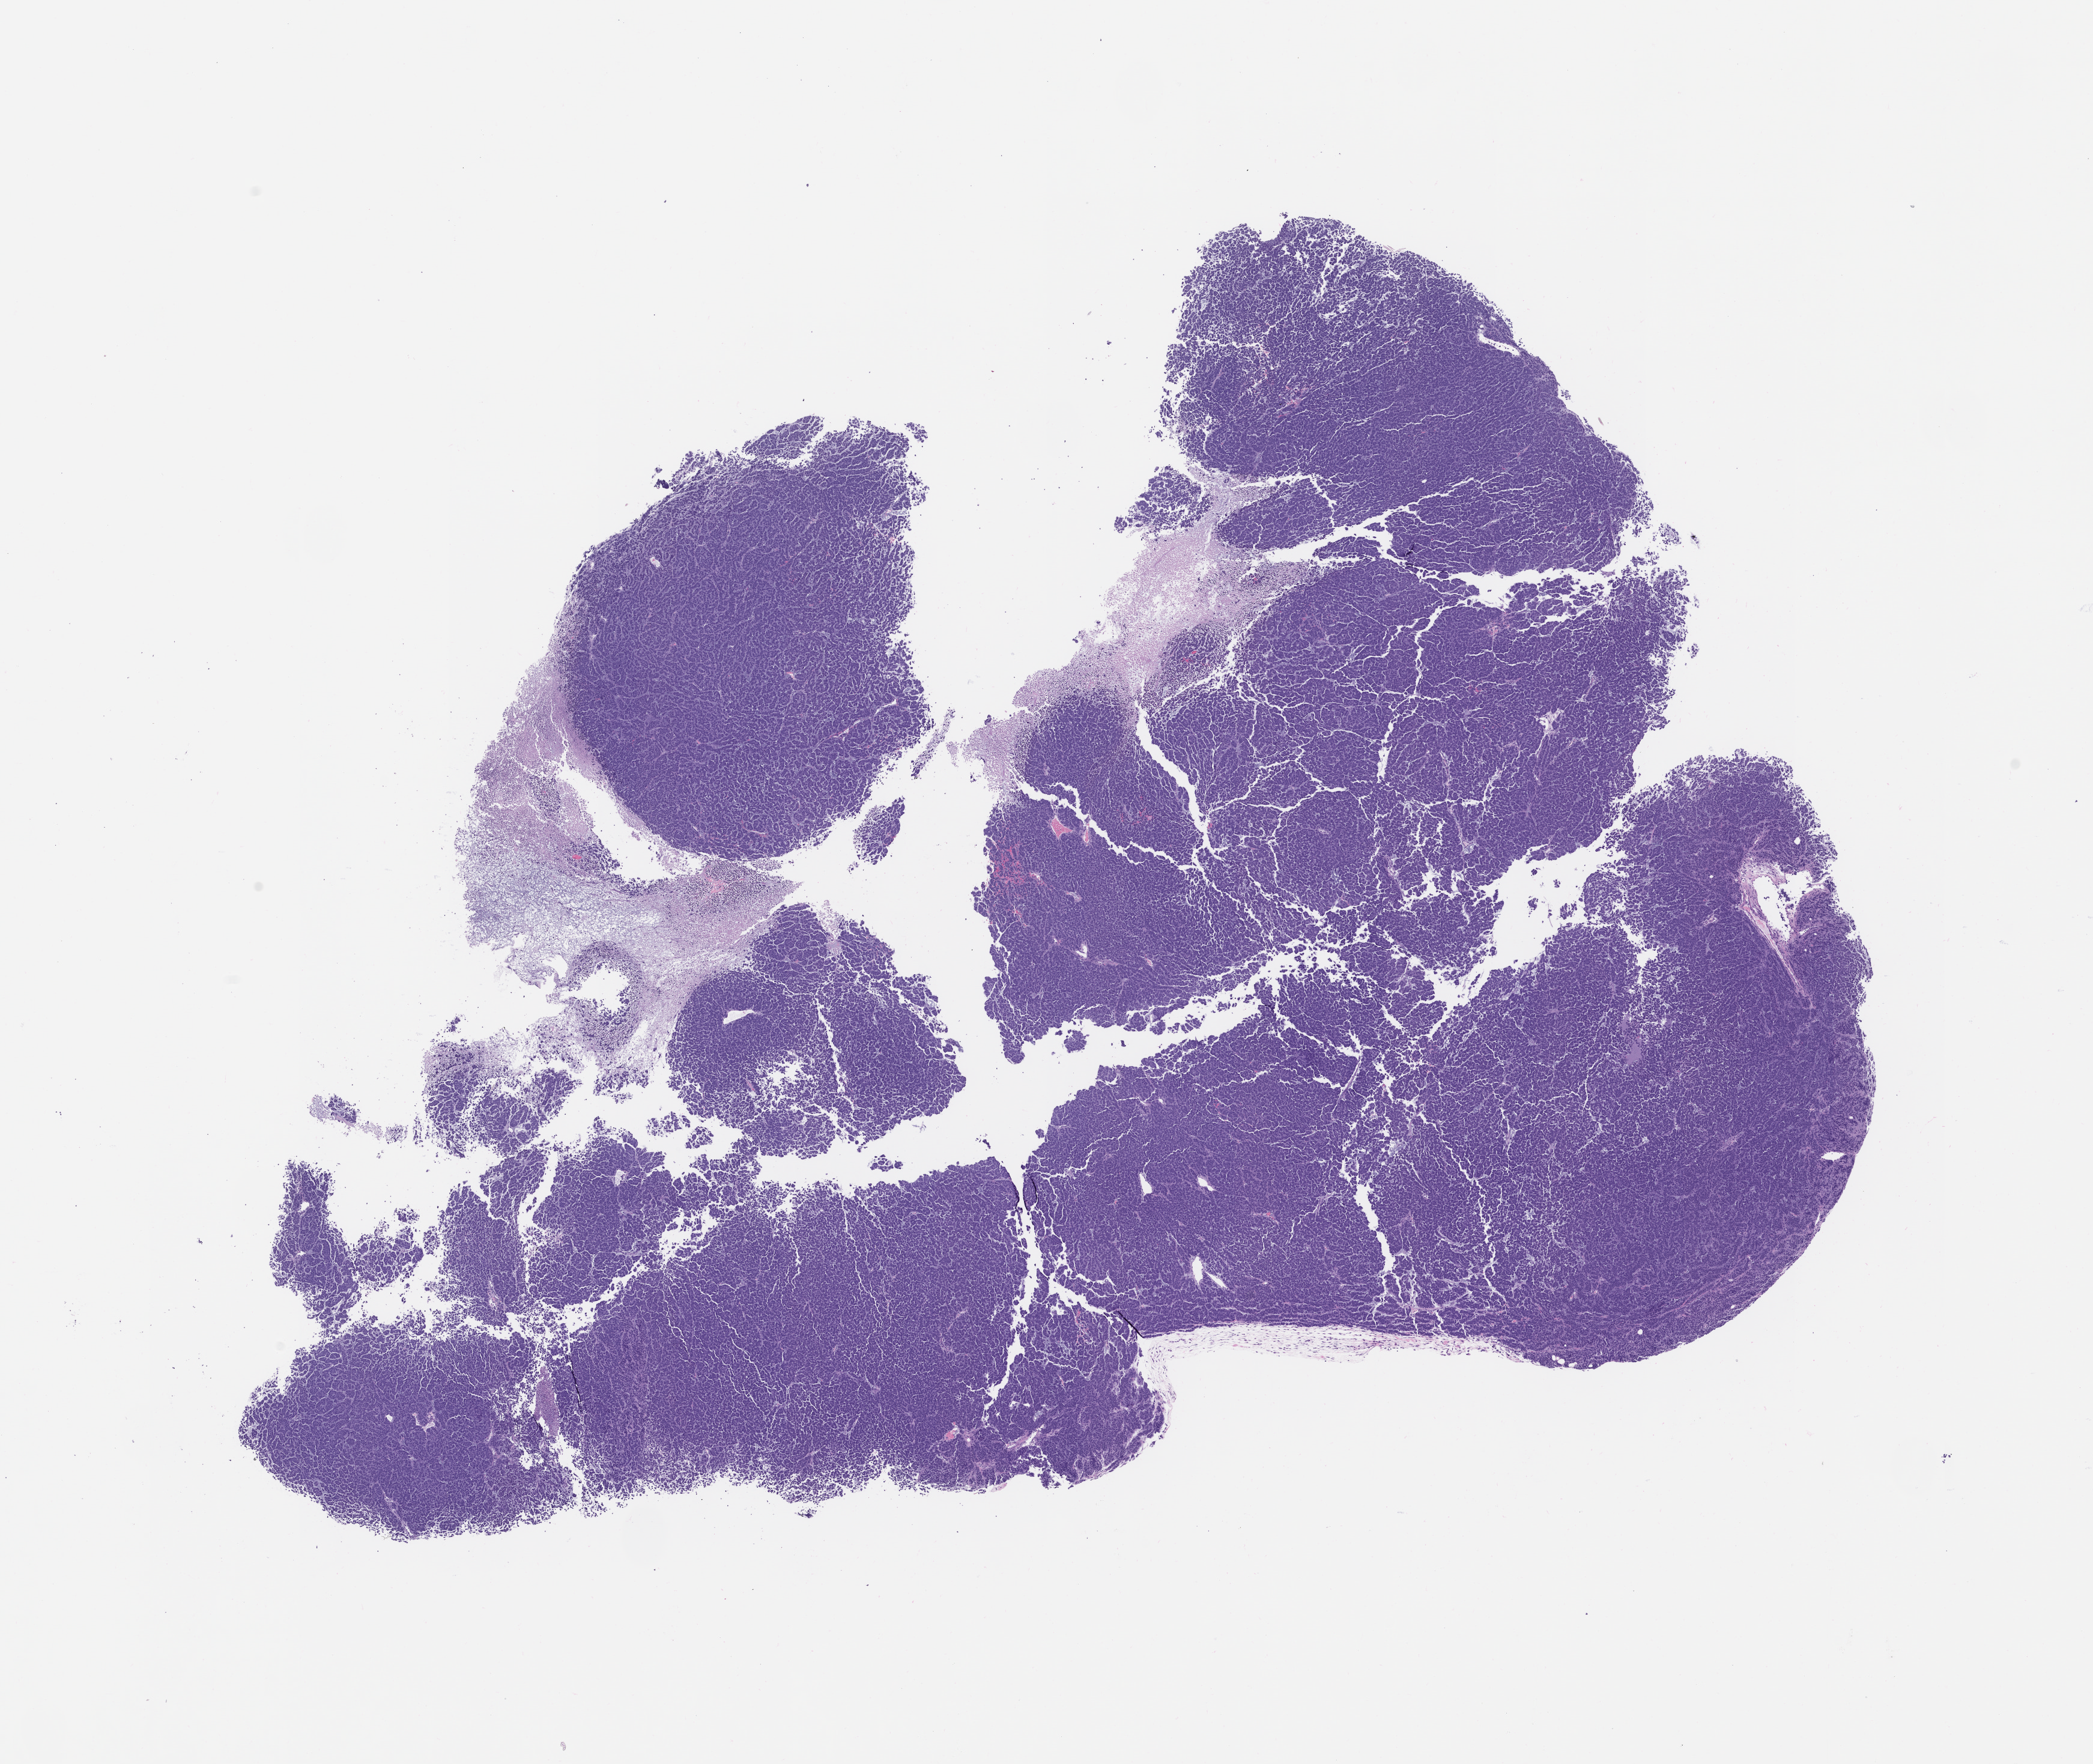
Whole-slide image, H&E: patient-derived xenograft (human tumor grown in a mouse), passage 1, whole scanned area (about 14.0 x 11.8 mm) shown as a low-resolution overview; FFPE section; tumor site category: ovary.
Originating patient diagnosis: Ovarian Carcinoma.